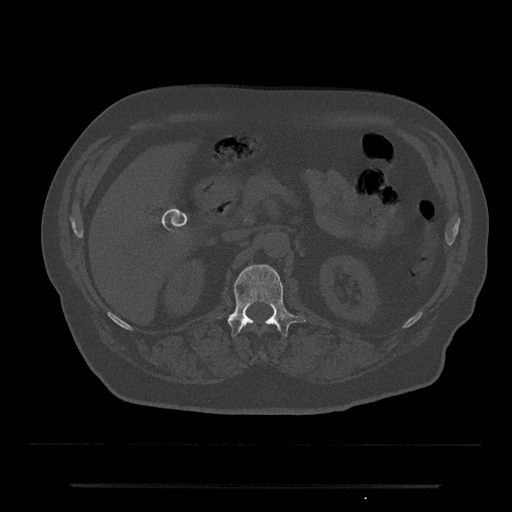
CT including the spine, one axial slice. Slice 546 of 797 in the series (ordered by position). Reconstruction kernel Br40s/3. Bone window (W 1800 / L 400 HU). 512 × 512 image matrix, field of view 434 × 434 mm. Male patient, age 80 years. Case-level facts recorded for this patient, not image findings: primary cancer: prostate.
Structures marked on this image (semi-automatic segmentation, software-assisted and operator-edited):
- L1 vertebra: bounding box (x1, y1, x2, y2) in pixels: (217, 264, 306, 336)